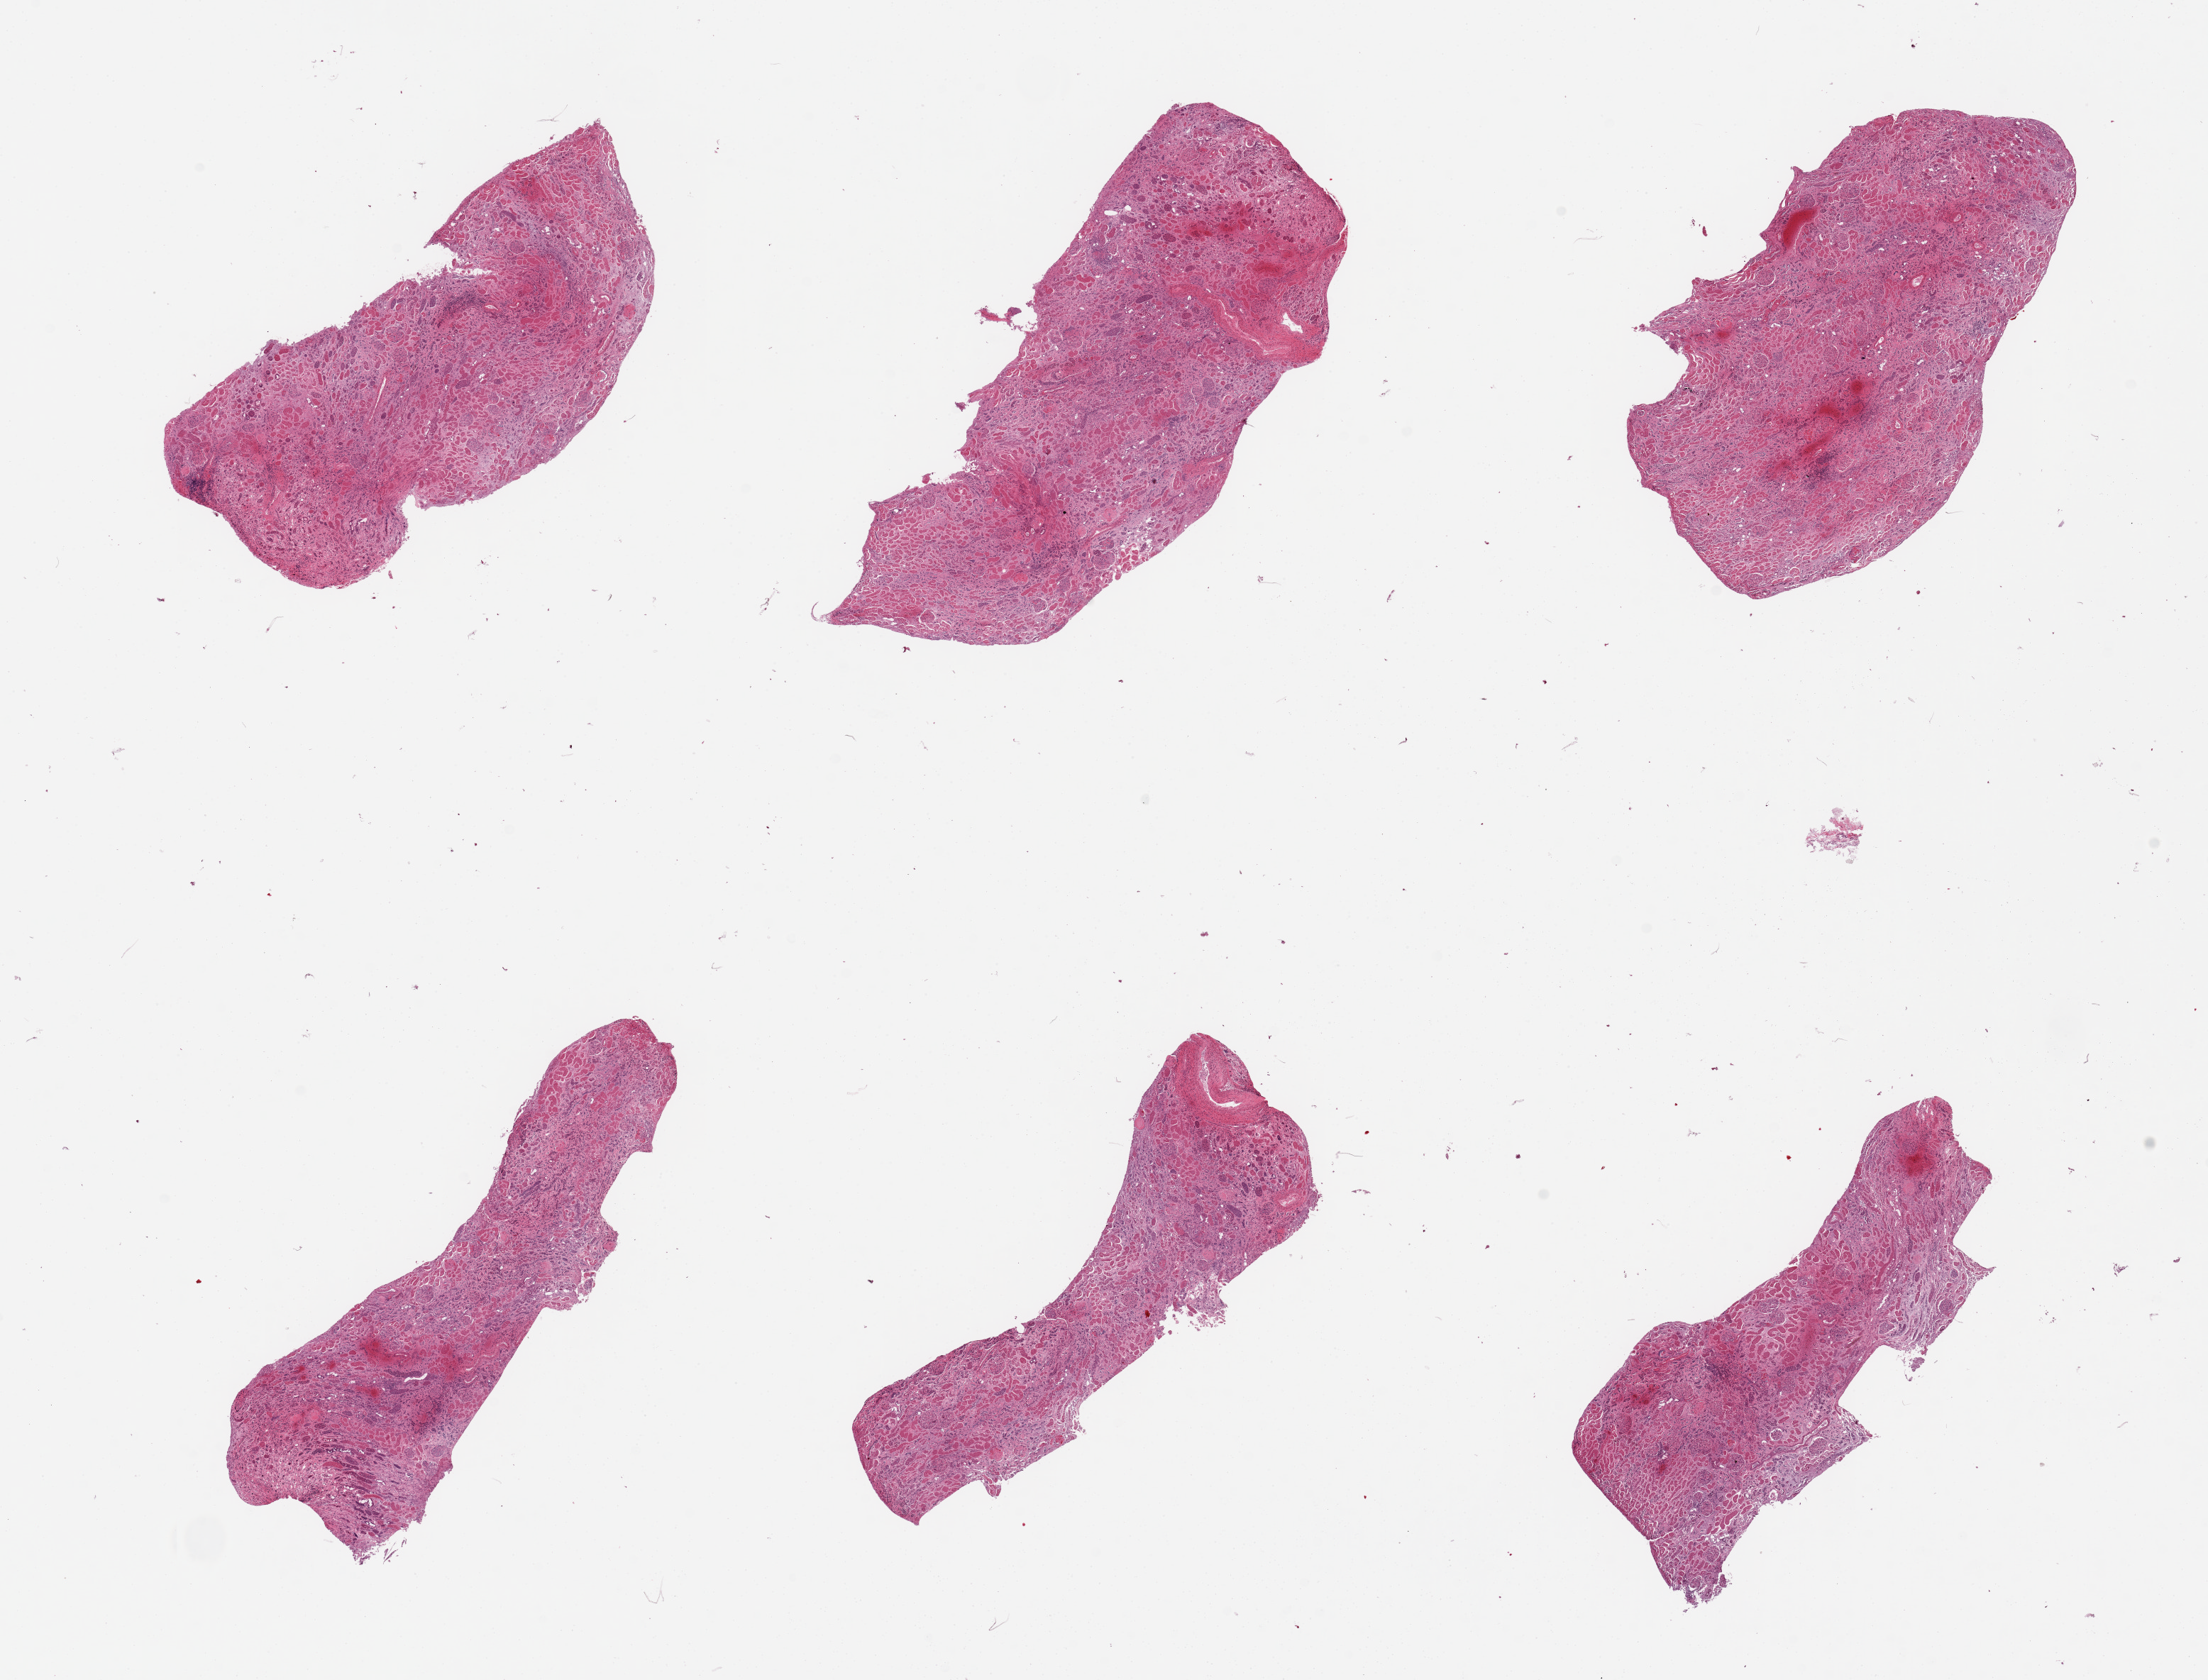
Haematoxylin and eosin whole-slide image, a low-resolution overview of the entire scanned area, about 24.6 x 18.7 mm, PAXgene-fixed paraffin-embedded (PFPE) section, section of renal cortex (target tissue), donor tissue sample. Donor: male.
* review note (as recorded): 6 pieces, badly autolyzed. Glomeruli prsent in all sections